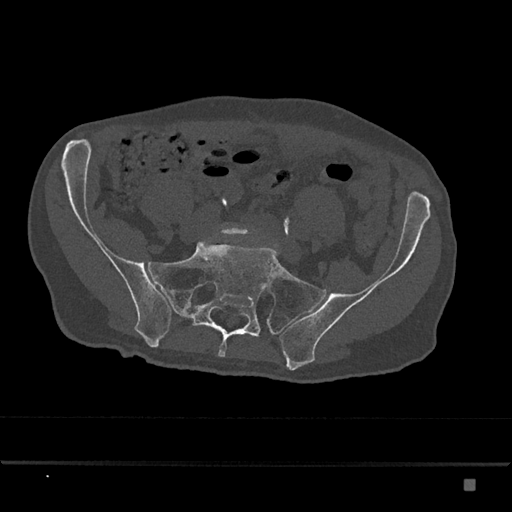
CT including the spine, one axial slice. Position 208 of 797 along the scan axis. Bone window (W 1800 / L 400 HU). 0.5 mm slice thickness. 512 × 512 image matrix. Patient: male, 72 years. From the clinical record (not read from this slice): primary cancer: prostate.
Structures marked on this image (semi-automatic segmentation, software-assisted and operator-edited):
- L5 vertebra: bounding box (x1, y1, x2, y2) in pixels: (221, 225, 253, 236)